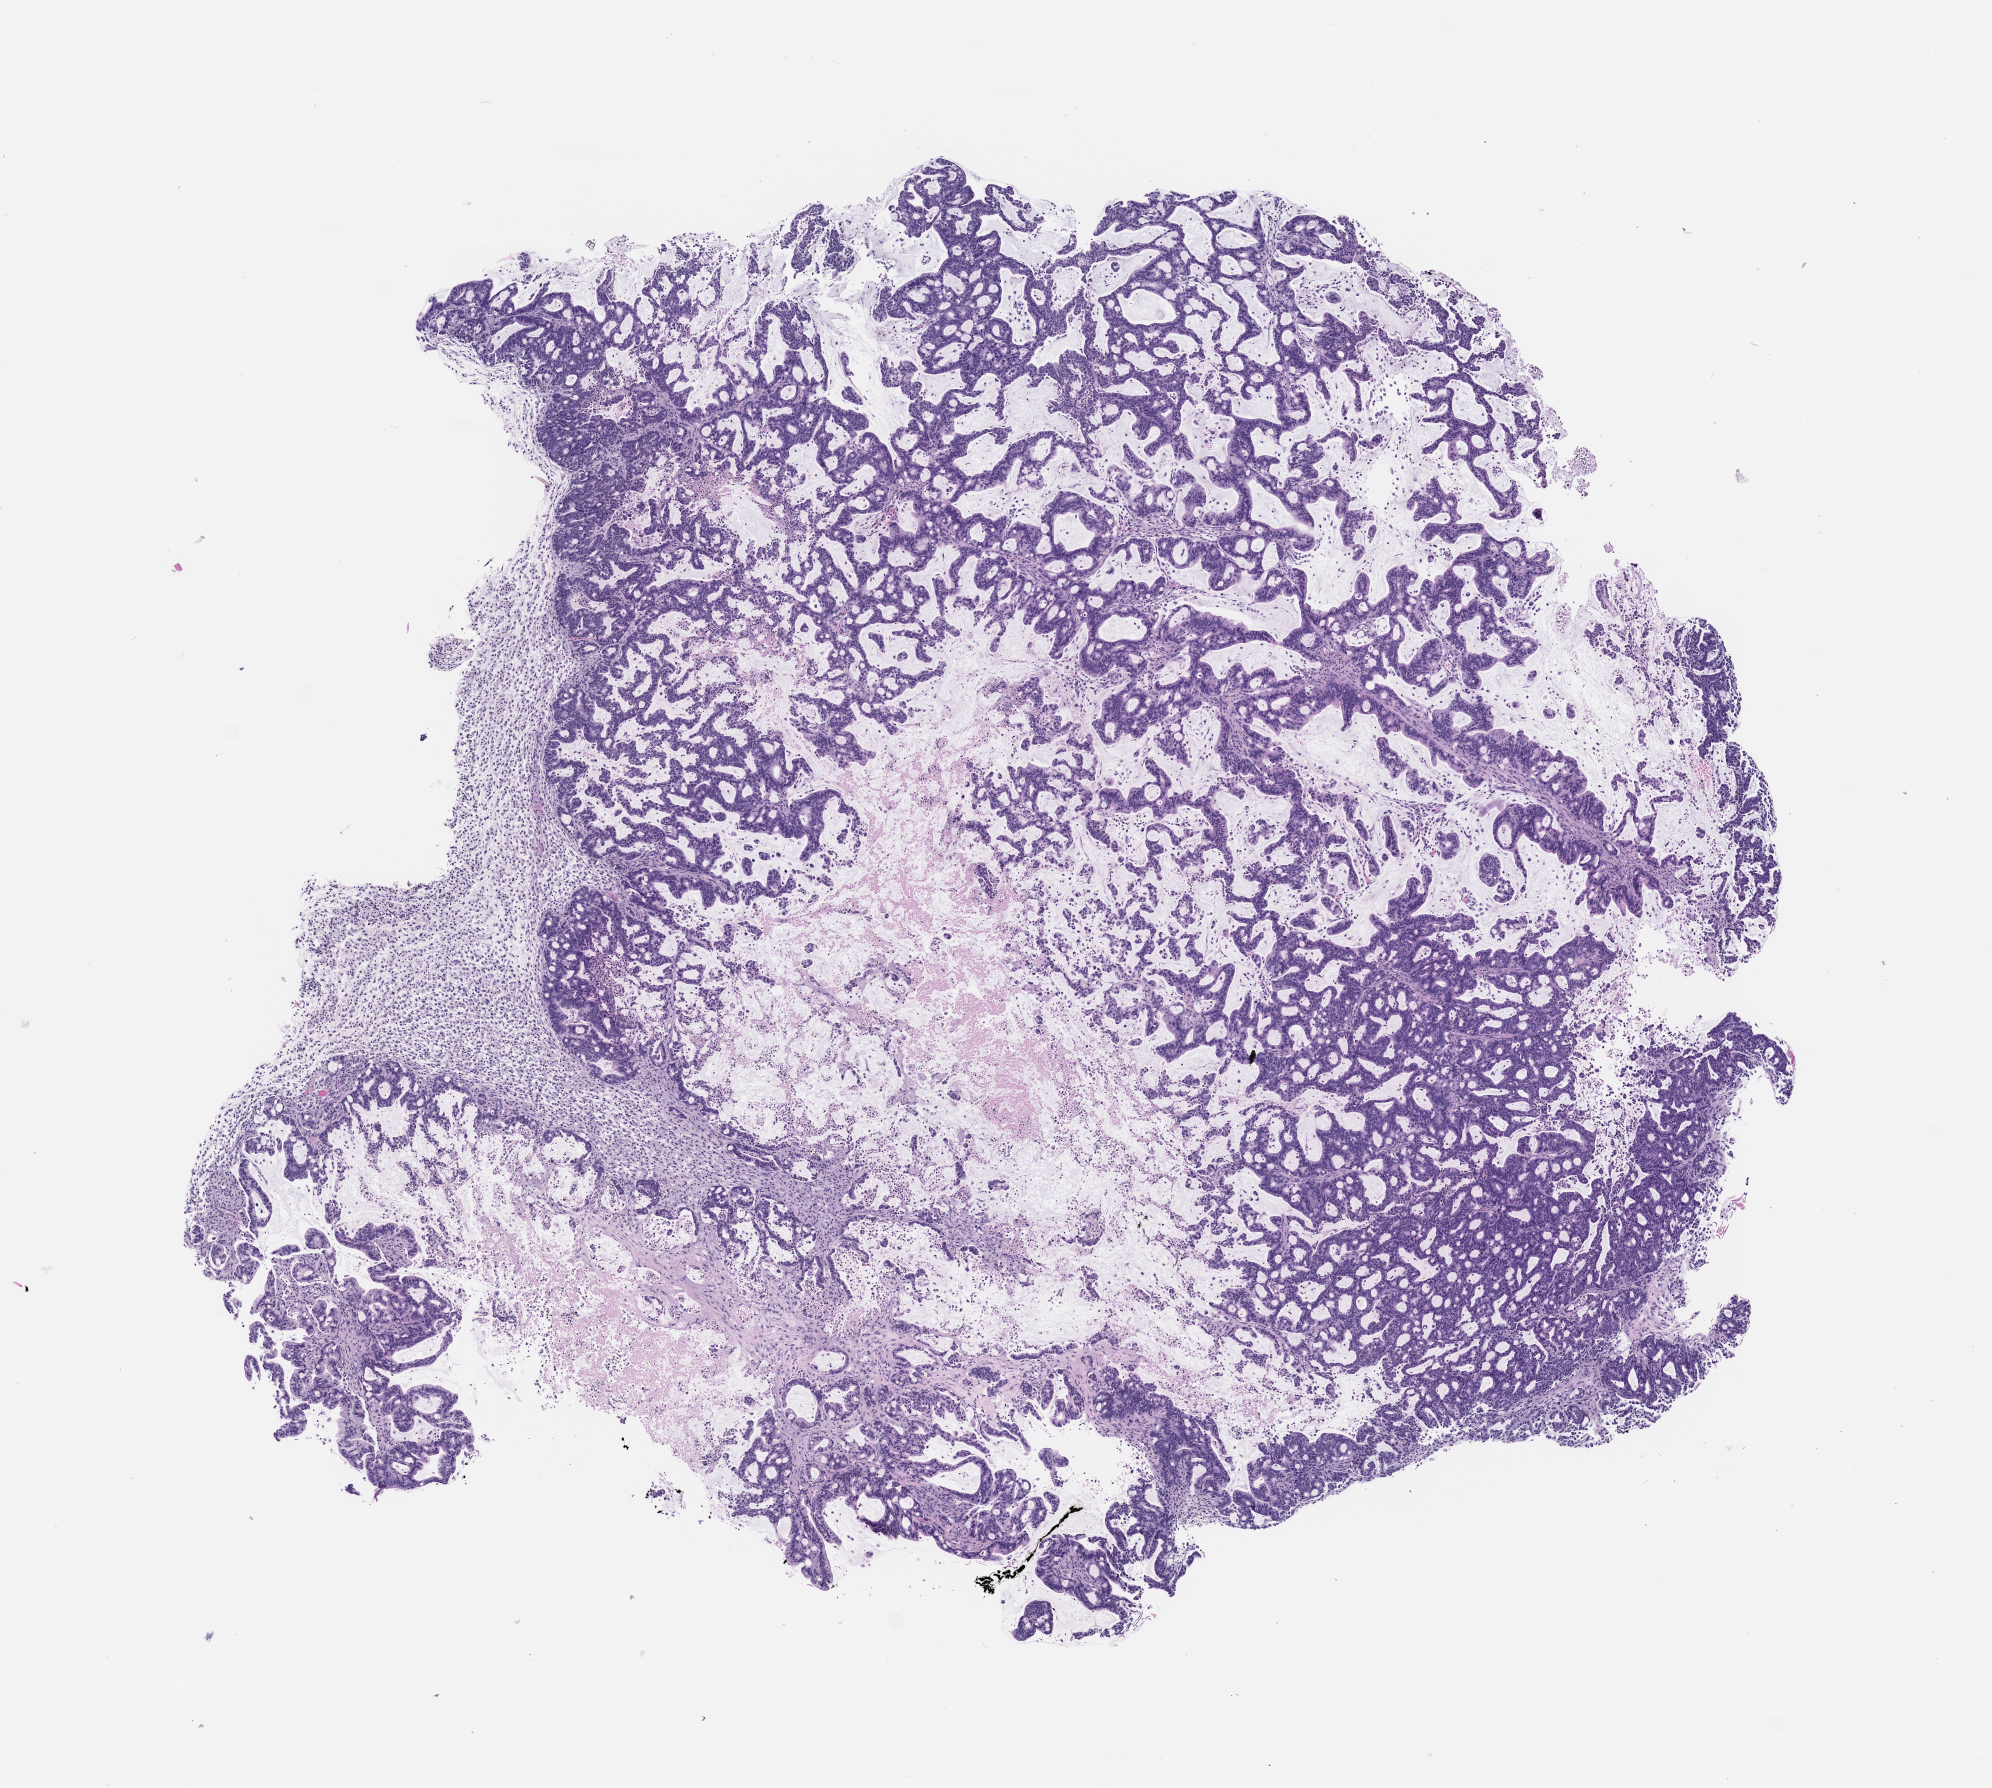
Hematoxylin and eosin (H&E) whole-slide image of a patient-derived xenograft (PDX) tumor grown in a mouse, passage 1, shown as a low-resolution overview of the whole scanned area (about 8.0 x 7.2 mm), FFPE section, originating tumor site category: colon.
• originating patient diagnosis: Colon Adenocarcinoma